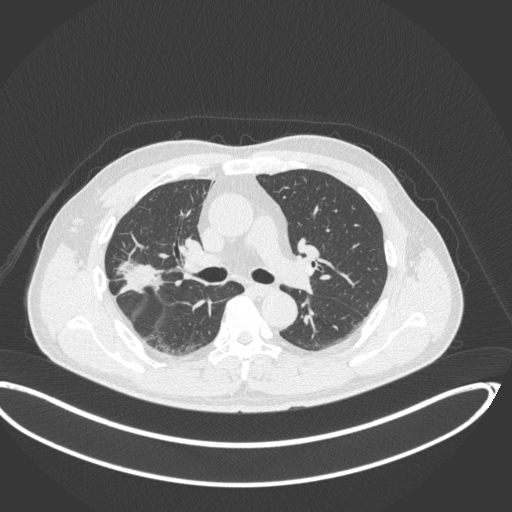
Chest CT, one axial slice. Slice 208 of 341 in the series (ordered by position). Reconstruction kernel B31f. Lung window (W 1500 / L -600 HU). 1 mm slice thickness. 512 × 512 image matrix, field of view 439 × 439 mm. Patient: male, 63 years. From the clinical record (not read from this slice): clinical TNM (as recorded): T1c N0 M0; histopathological grade: G2-3.
Structures marked on this image (rectangle marked by the reading radiologist):
- lung tumour (recorded histology: adenocarcinoma): box from (x=116, y=254) to (x=169, y=300) px